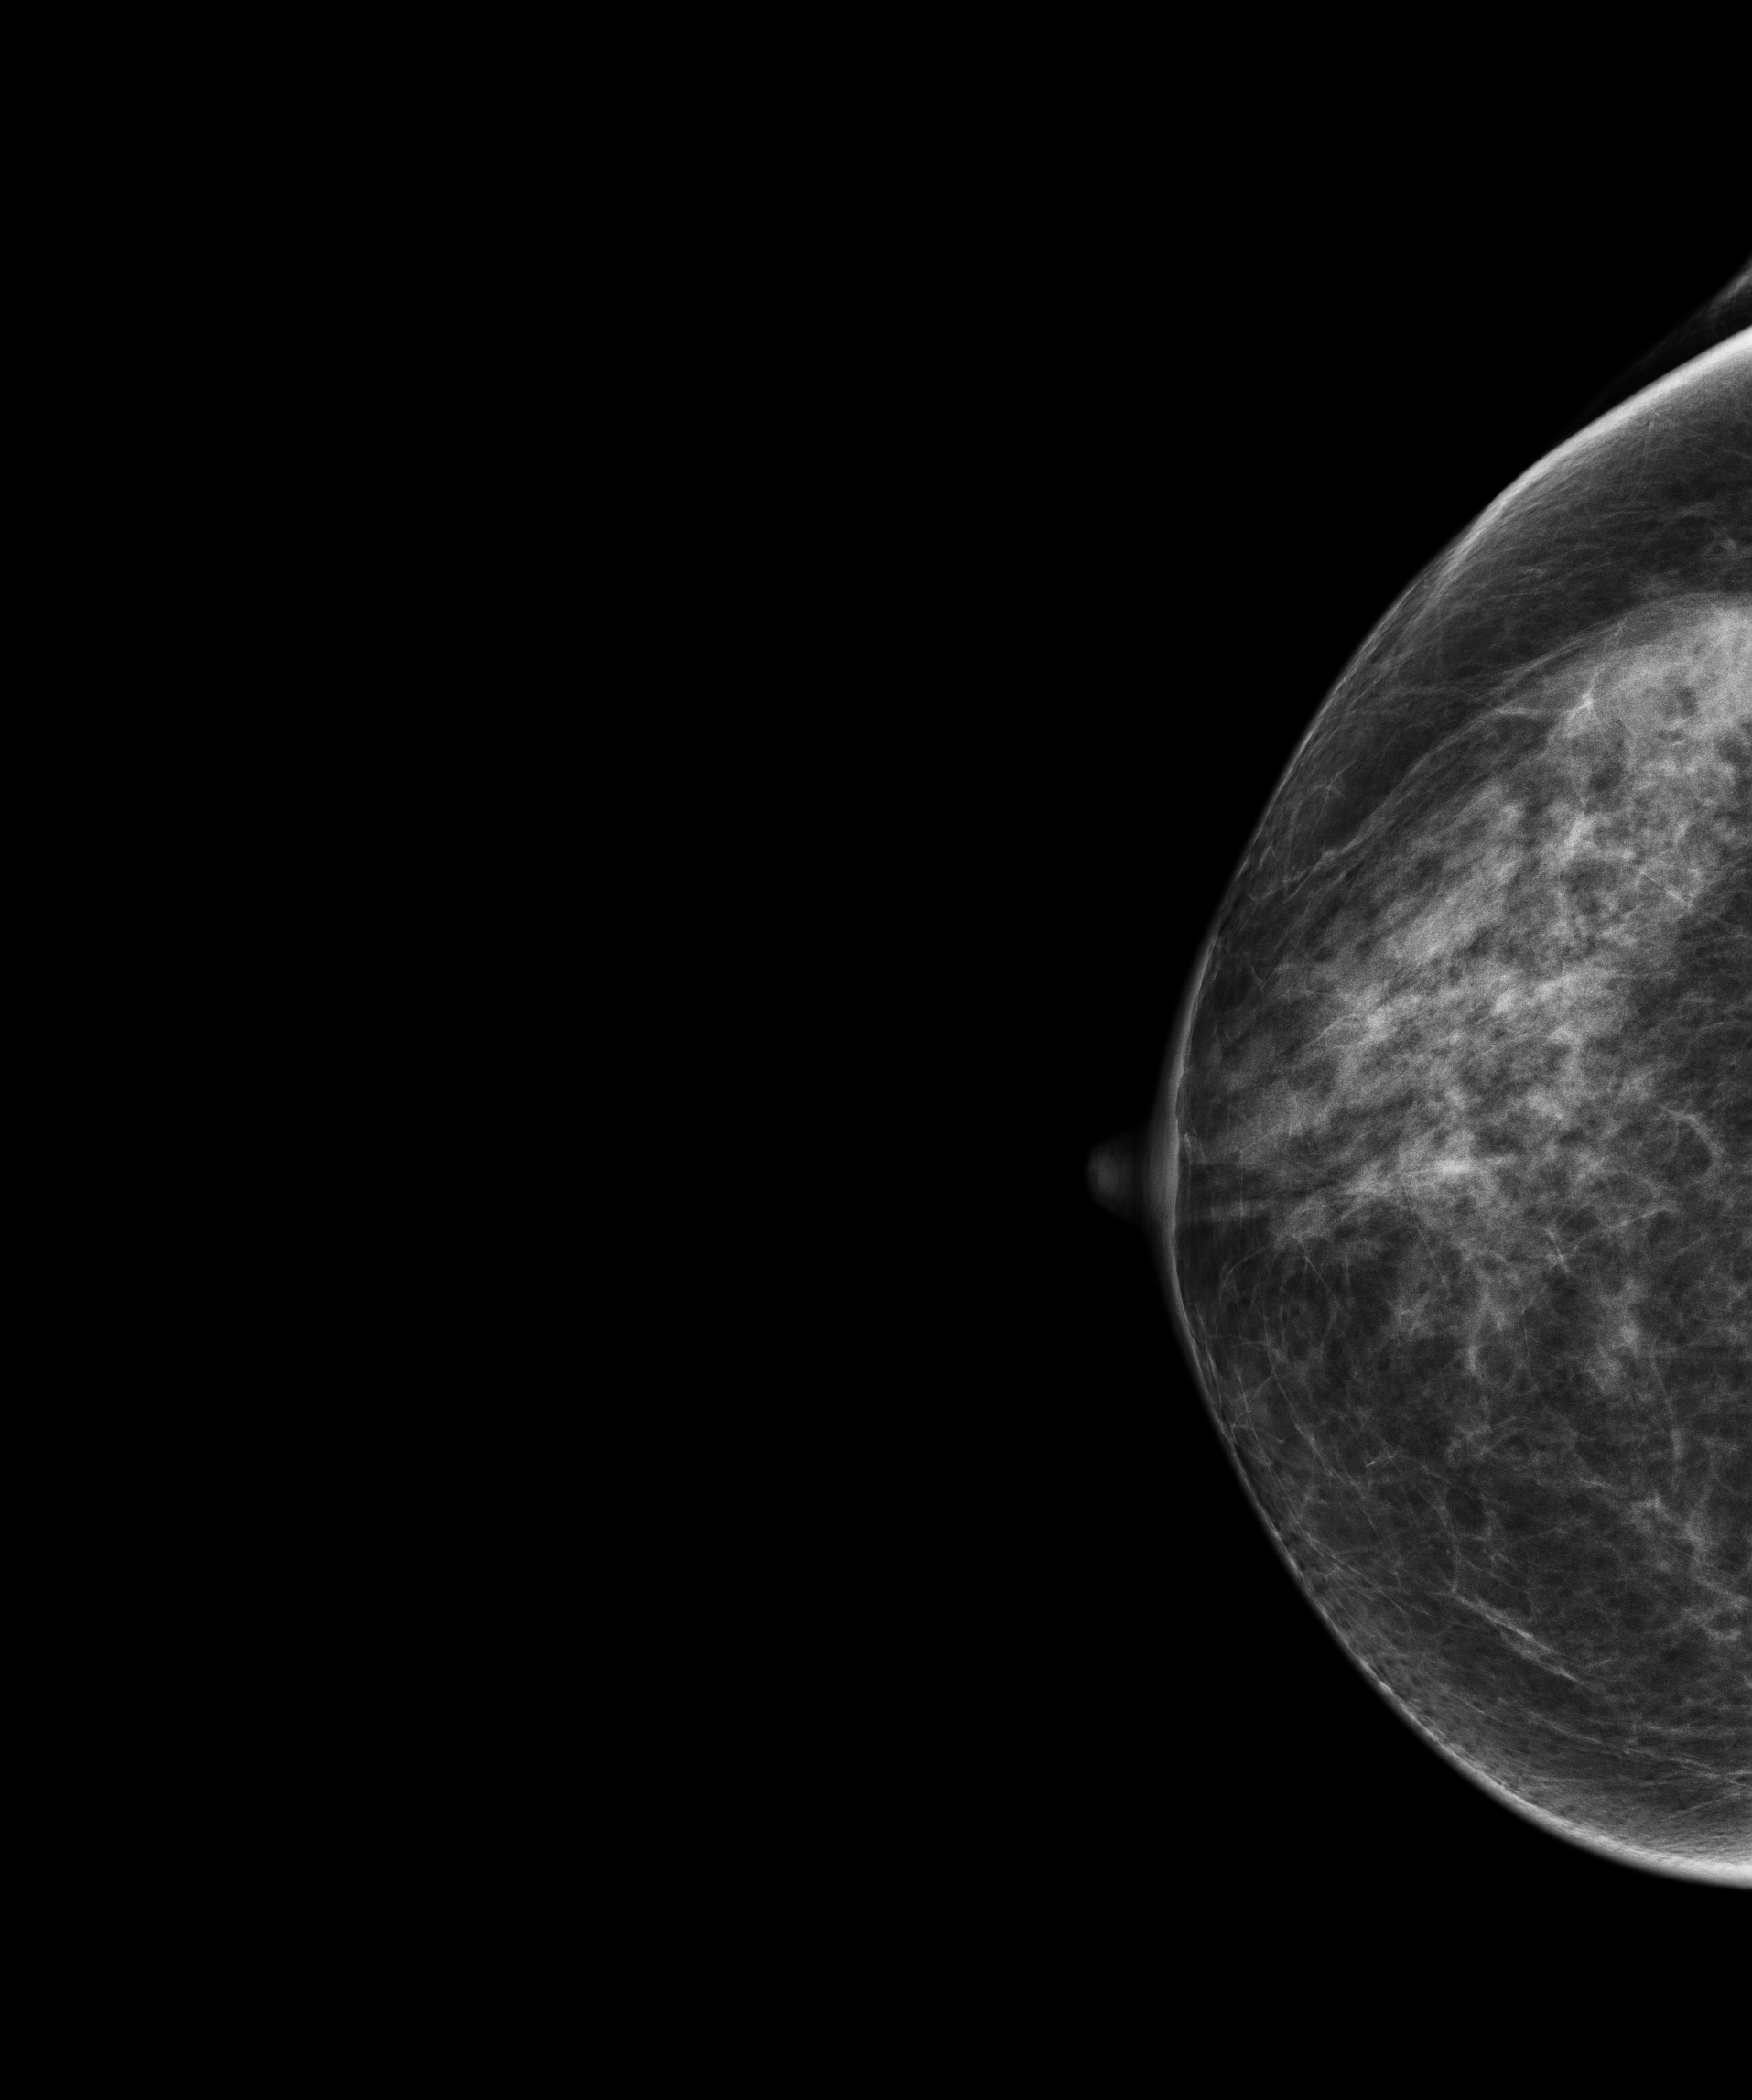
Digital mammogram (FFDM), right breast, cranio-caudal projection, annual screening mammography examination, compressed breast thickness 54 mm. Female patient, age 61 years.
BI-RADS breast density category at the screening exam (both breasts, scale 1–4): 3. Final BI-RADS category for the screening round (tomosynthesis exam, both breasts): category 1. Recall: no recall after this screen.